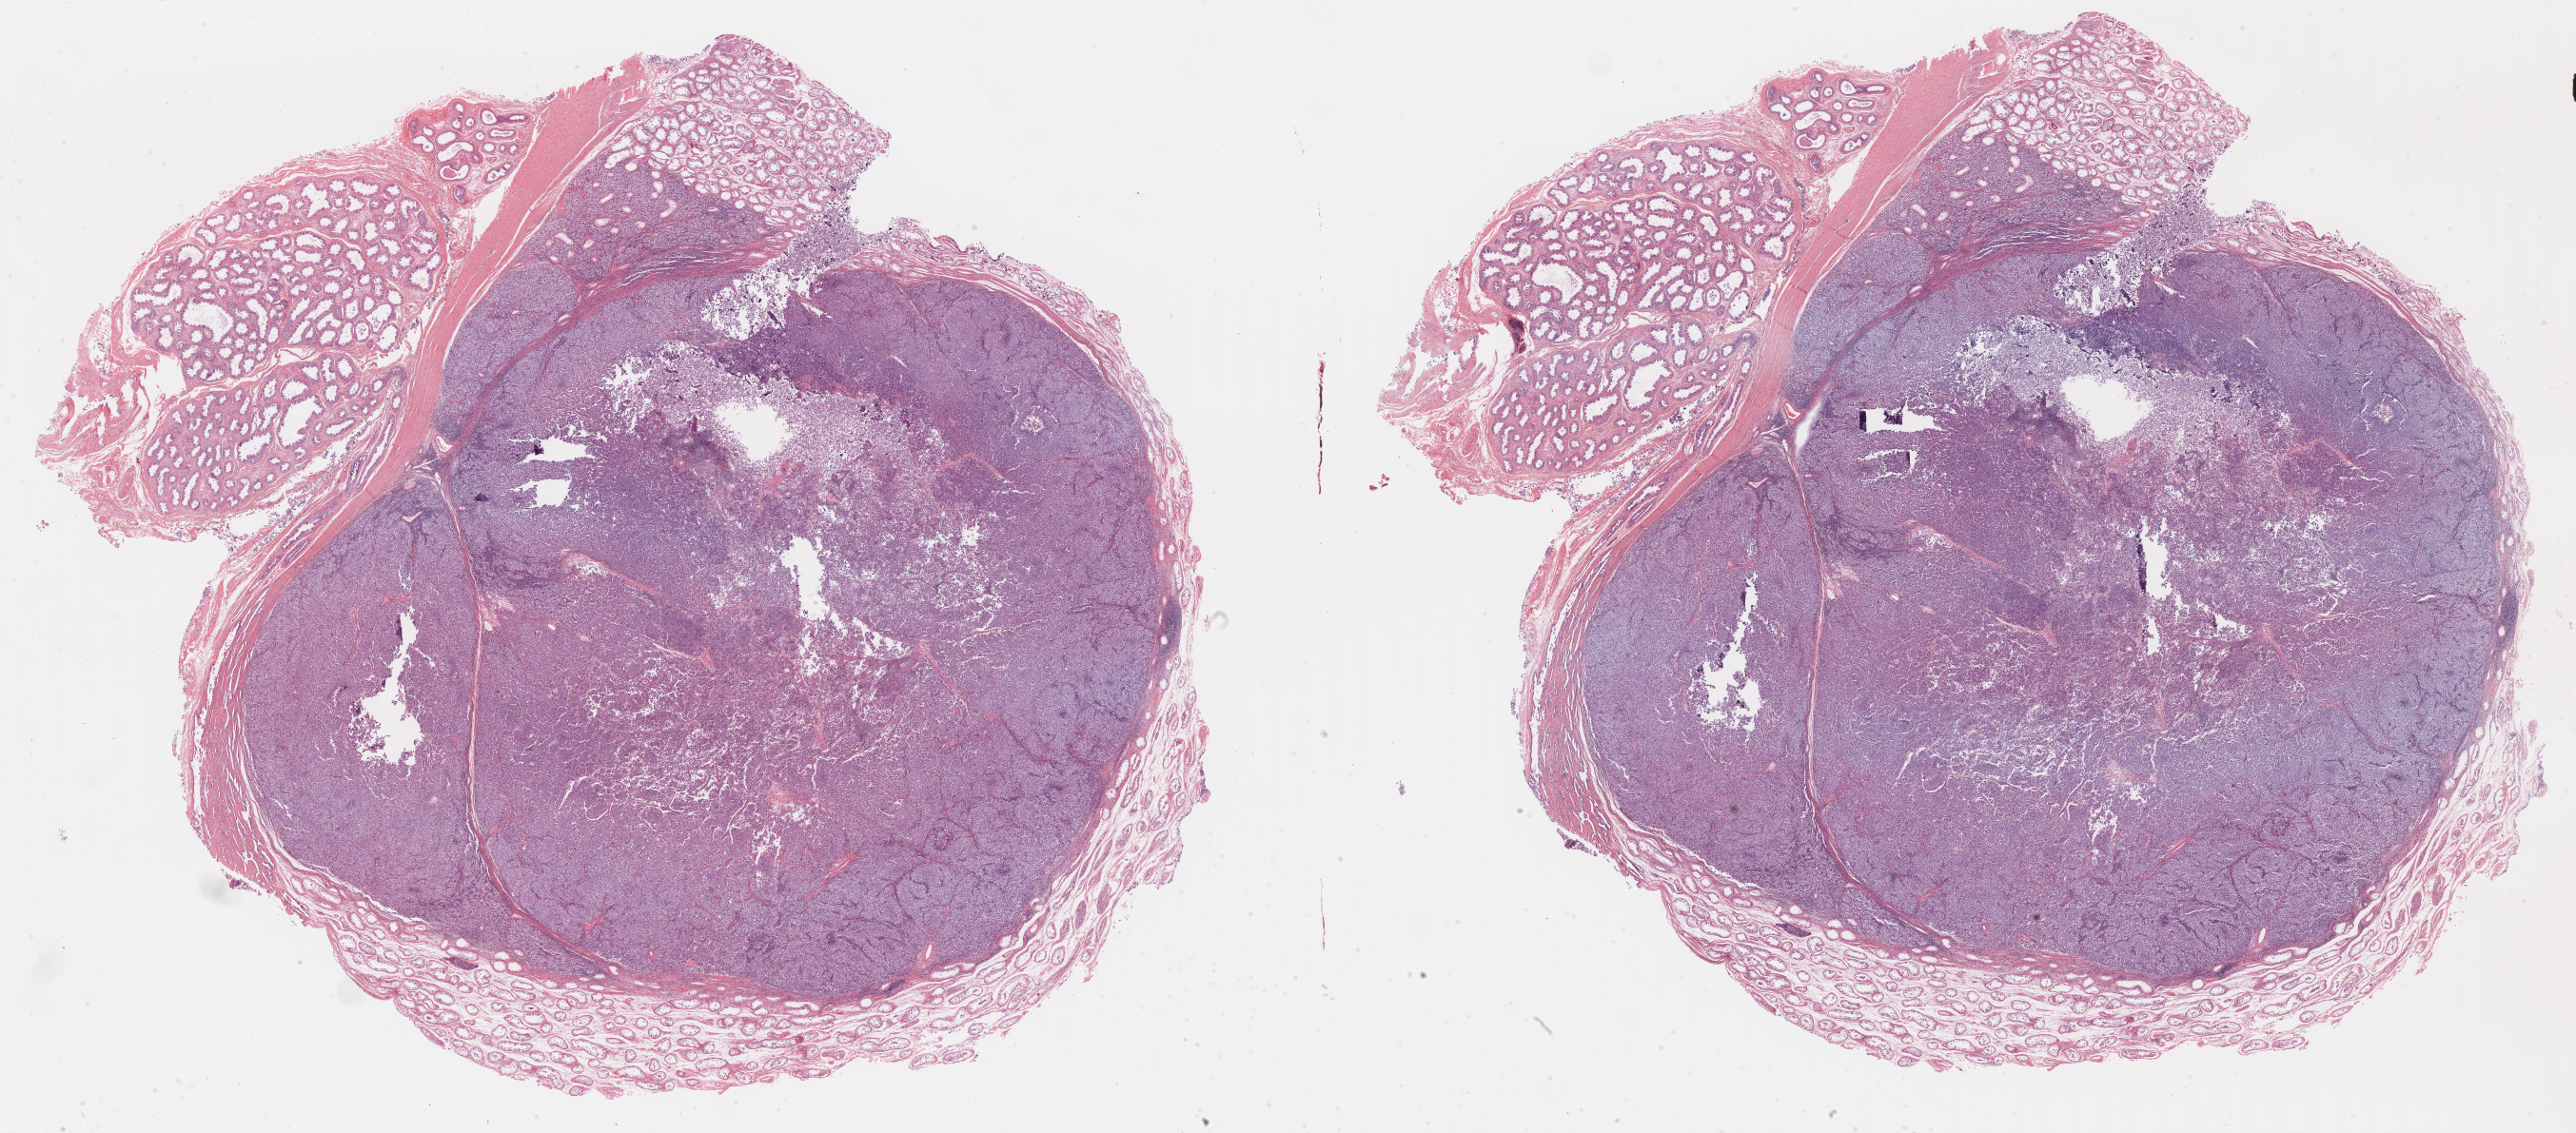
H&E whole-slide image — a low-resolution overview of the entire scanned area, about 43.8 x 19.3 mm (slide scanned at 40x). Formalin-fixed paraffin-embedded (FFPE) diagnostic section. Testis, primary tumour sample. Male patient; age at initial diagnosis 40 years.
• AJCC pathologic stage: IA (6th edition)
• diagnosis: Seminoma, NOS